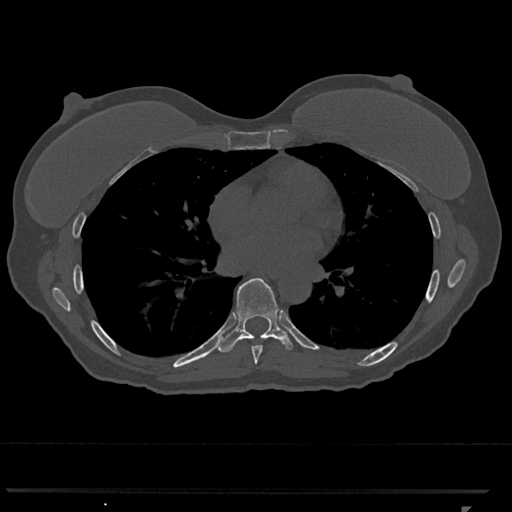
CT including the spine, one axial slice; position 681 of 793 along the scan axis; reconstruction kernel Br40s/3; 120 kVp; bone window (W 1800 / L 400 HU); 0.5 mm slice thickness; 512 × 512 image matrix, field of view 380 × 380 mm. Female patient, age 62 years. Case-level facts recorded for this patient, not image findings: primary cancer: renal.
Outlined on this slice (semi-automatically segmented with operator editing):
- T7 vertebra: bounding box [x1, y1, x2, y2] px = [252, 345, 262, 365]
- T8 vertebra: [218, 278, 293, 353]